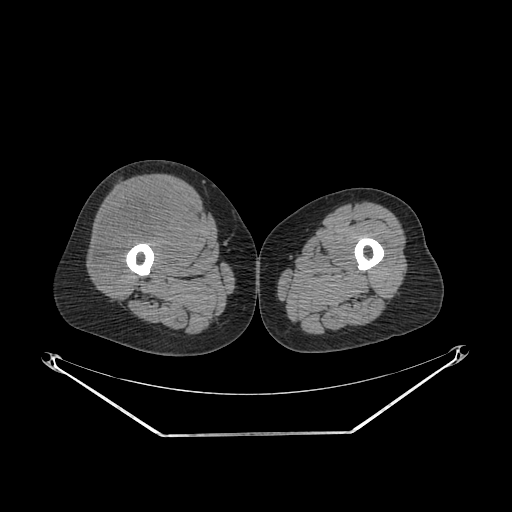
CT of an extremity soft-tissue mass (from a PET/CT study), one axial slice. Position 242 of 311 along the scan axis. Soft-tissue window (W 400 / L 40 HU). 3.75 mm slice thickness. 512 × 512 image matrix, field of view 500 × 500 mm. Female patient. Case-level facts recorded for this patient, not image findings: histological type: pleiomorphic undifferentiated sarcoma; grade: high; site of the primary tumour: right quadricep.
Structures marked on this image (expert contour drawn on MRI and transferred to this co-registered scan by the dataset authors):
- tumour plus oedema (research contour): box from (x=96, y=190) to (x=193, y=282) px
- tumour (research contour): (x=96, y=190)–(x=193, y=282)